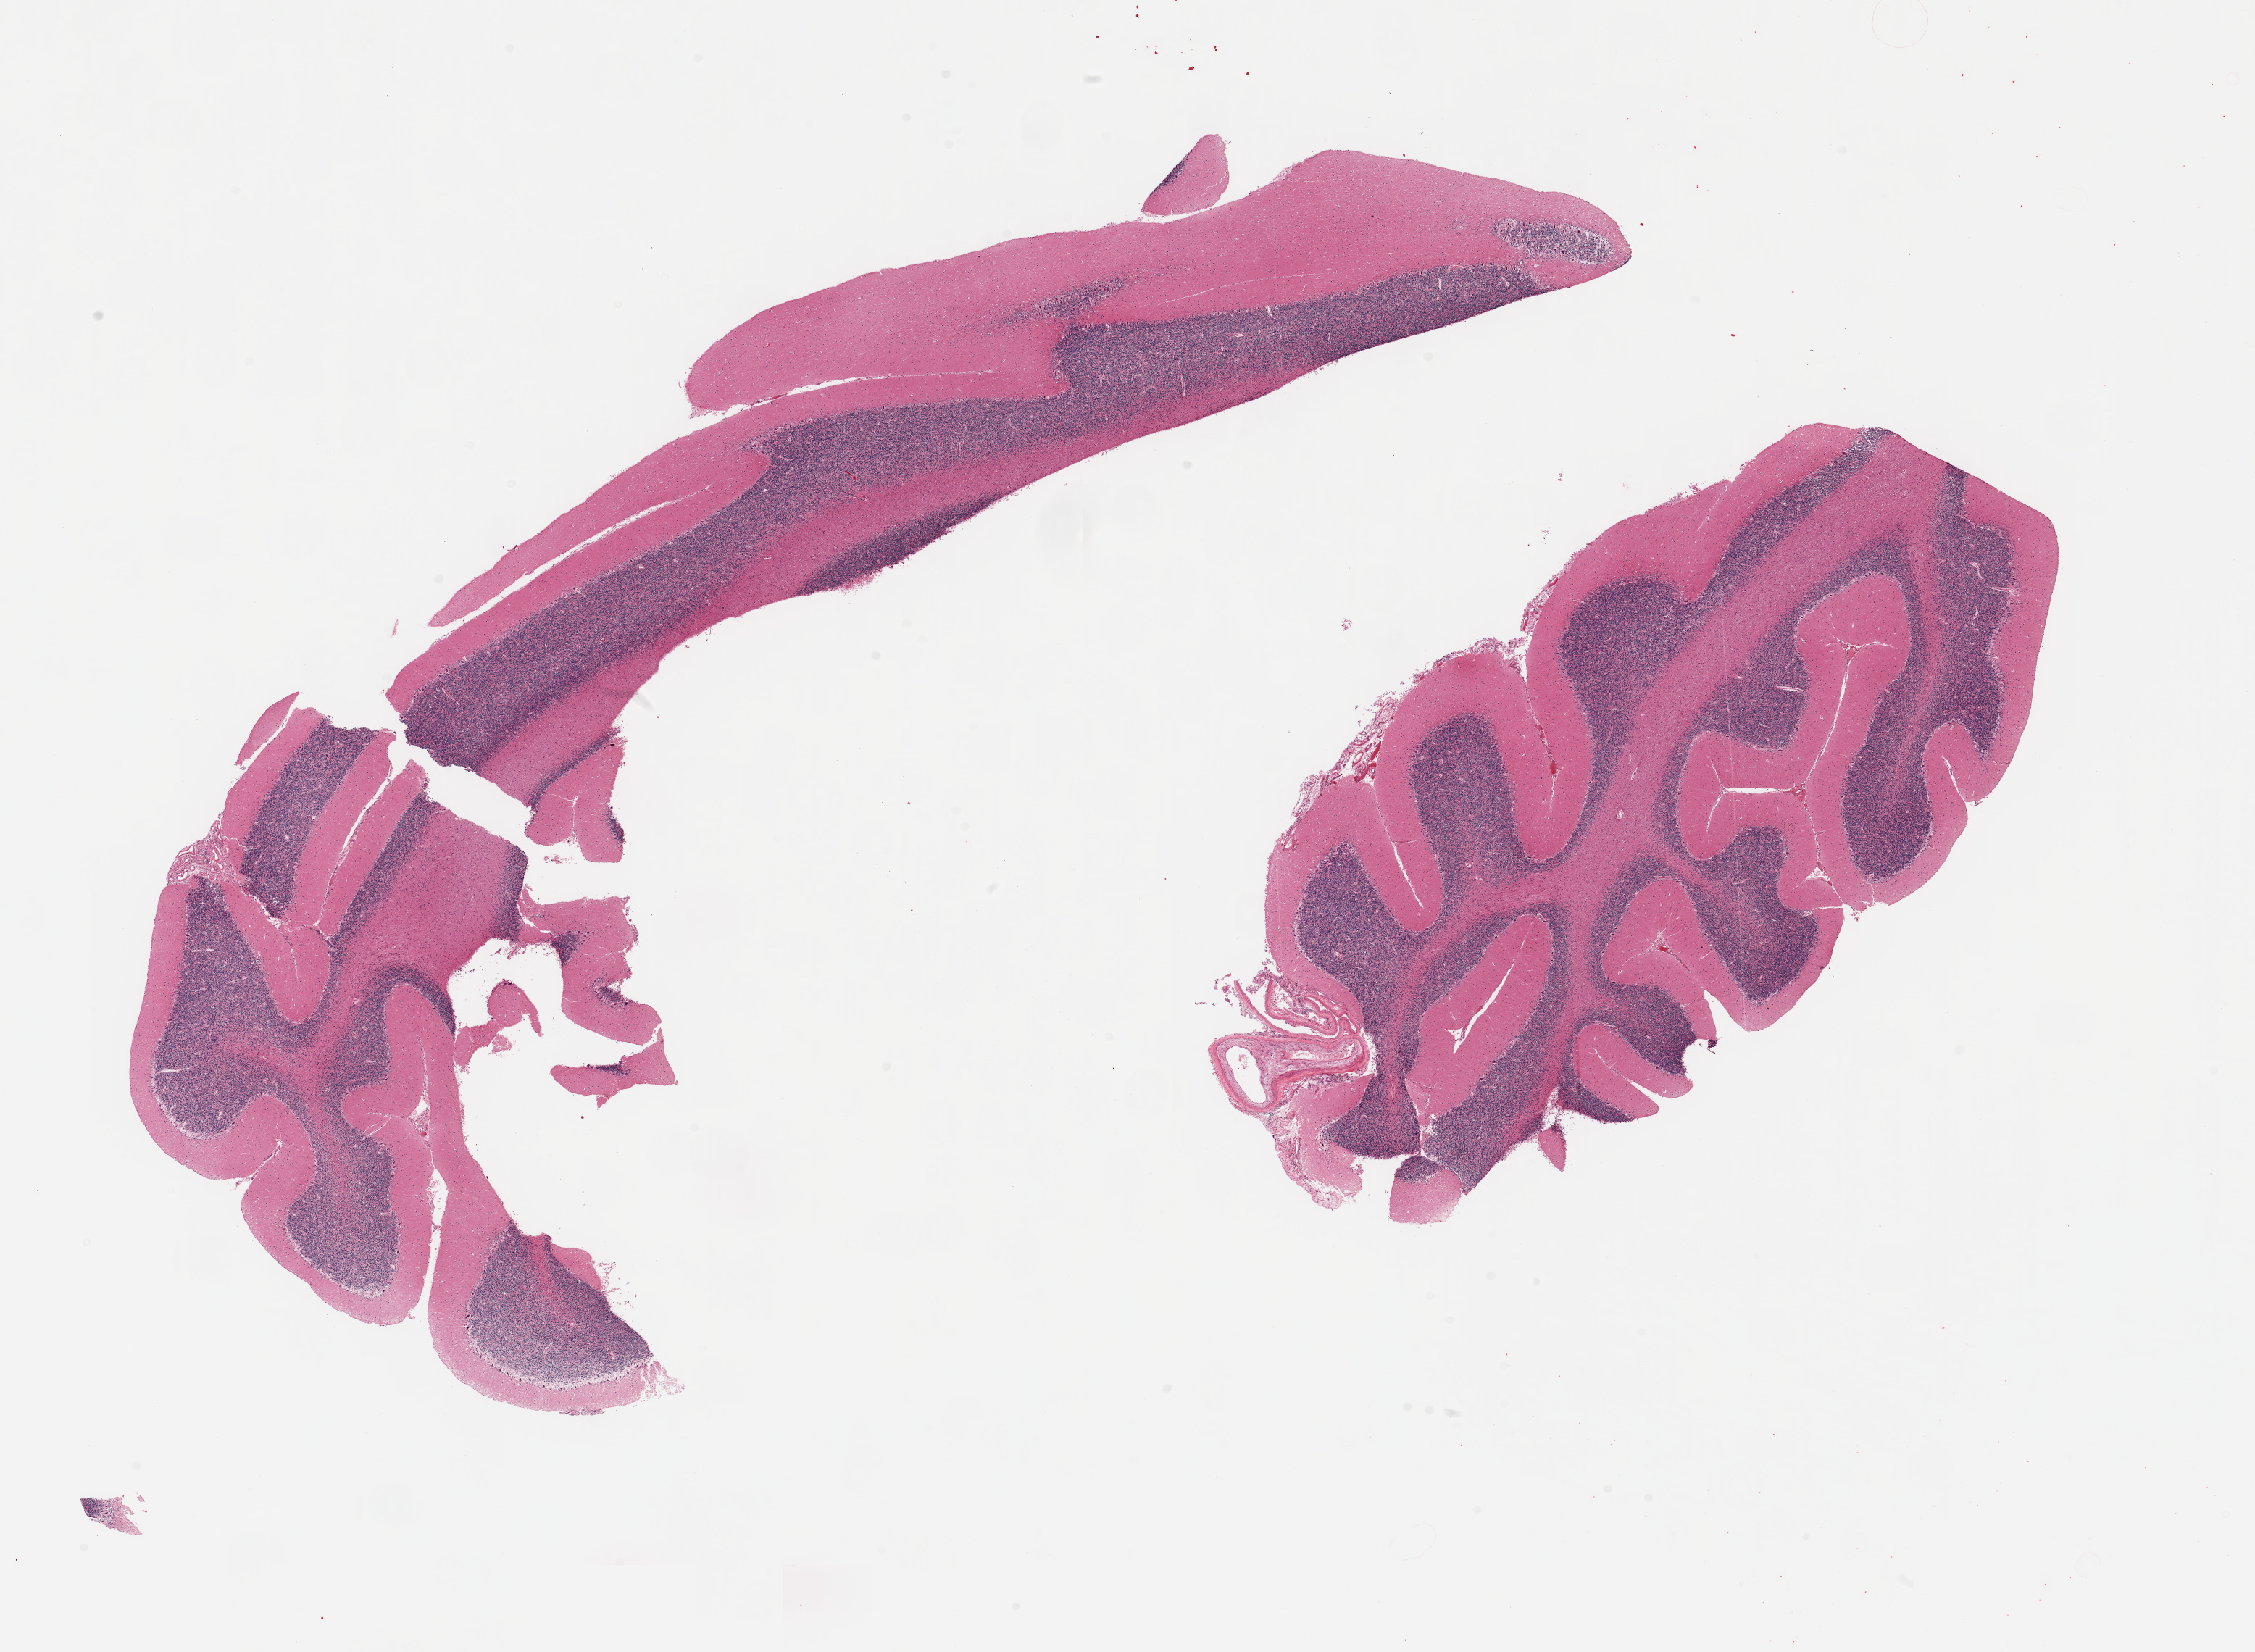
Whole-slide image, haematoxylin and eosin stain — shown as a low-resolution overview of the whole scanned area (about 24.6 x 18.0 mm), PAXgene-fixed paraffin-embedded (PFPE) section, section of cerebellum (target tissue), donor tissue sample. Donor sex: male.
Reviewer comment on this tissue sample: 2 pieces, no abnormalities.